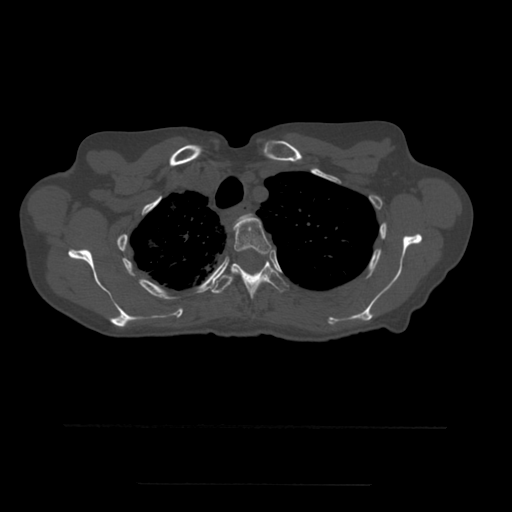
CT including the spine, one axial slice. Slice 415 of 544 in the series (ordered by position). Bone window (W 1800 / L 400 HU). 1.25 mm slice thickness. 512 × 512 image matrix, field of view 350 × 350 mm. Patient age 58 years. Case-level facts recorded for this patient, not image findings: primary cancer: lung.
Annotated regions visible in this slice (semi-automatic segmentation, software-assisted and operator-edited):
- T2 vertebra: box from (x=235, y=214) to (x=253, y=227) px
- T3 vertebra: (x=231, y=217)–(x=274, y=276)
- T4 vertebra: (x=211, y=254)–(x=290, y=299)